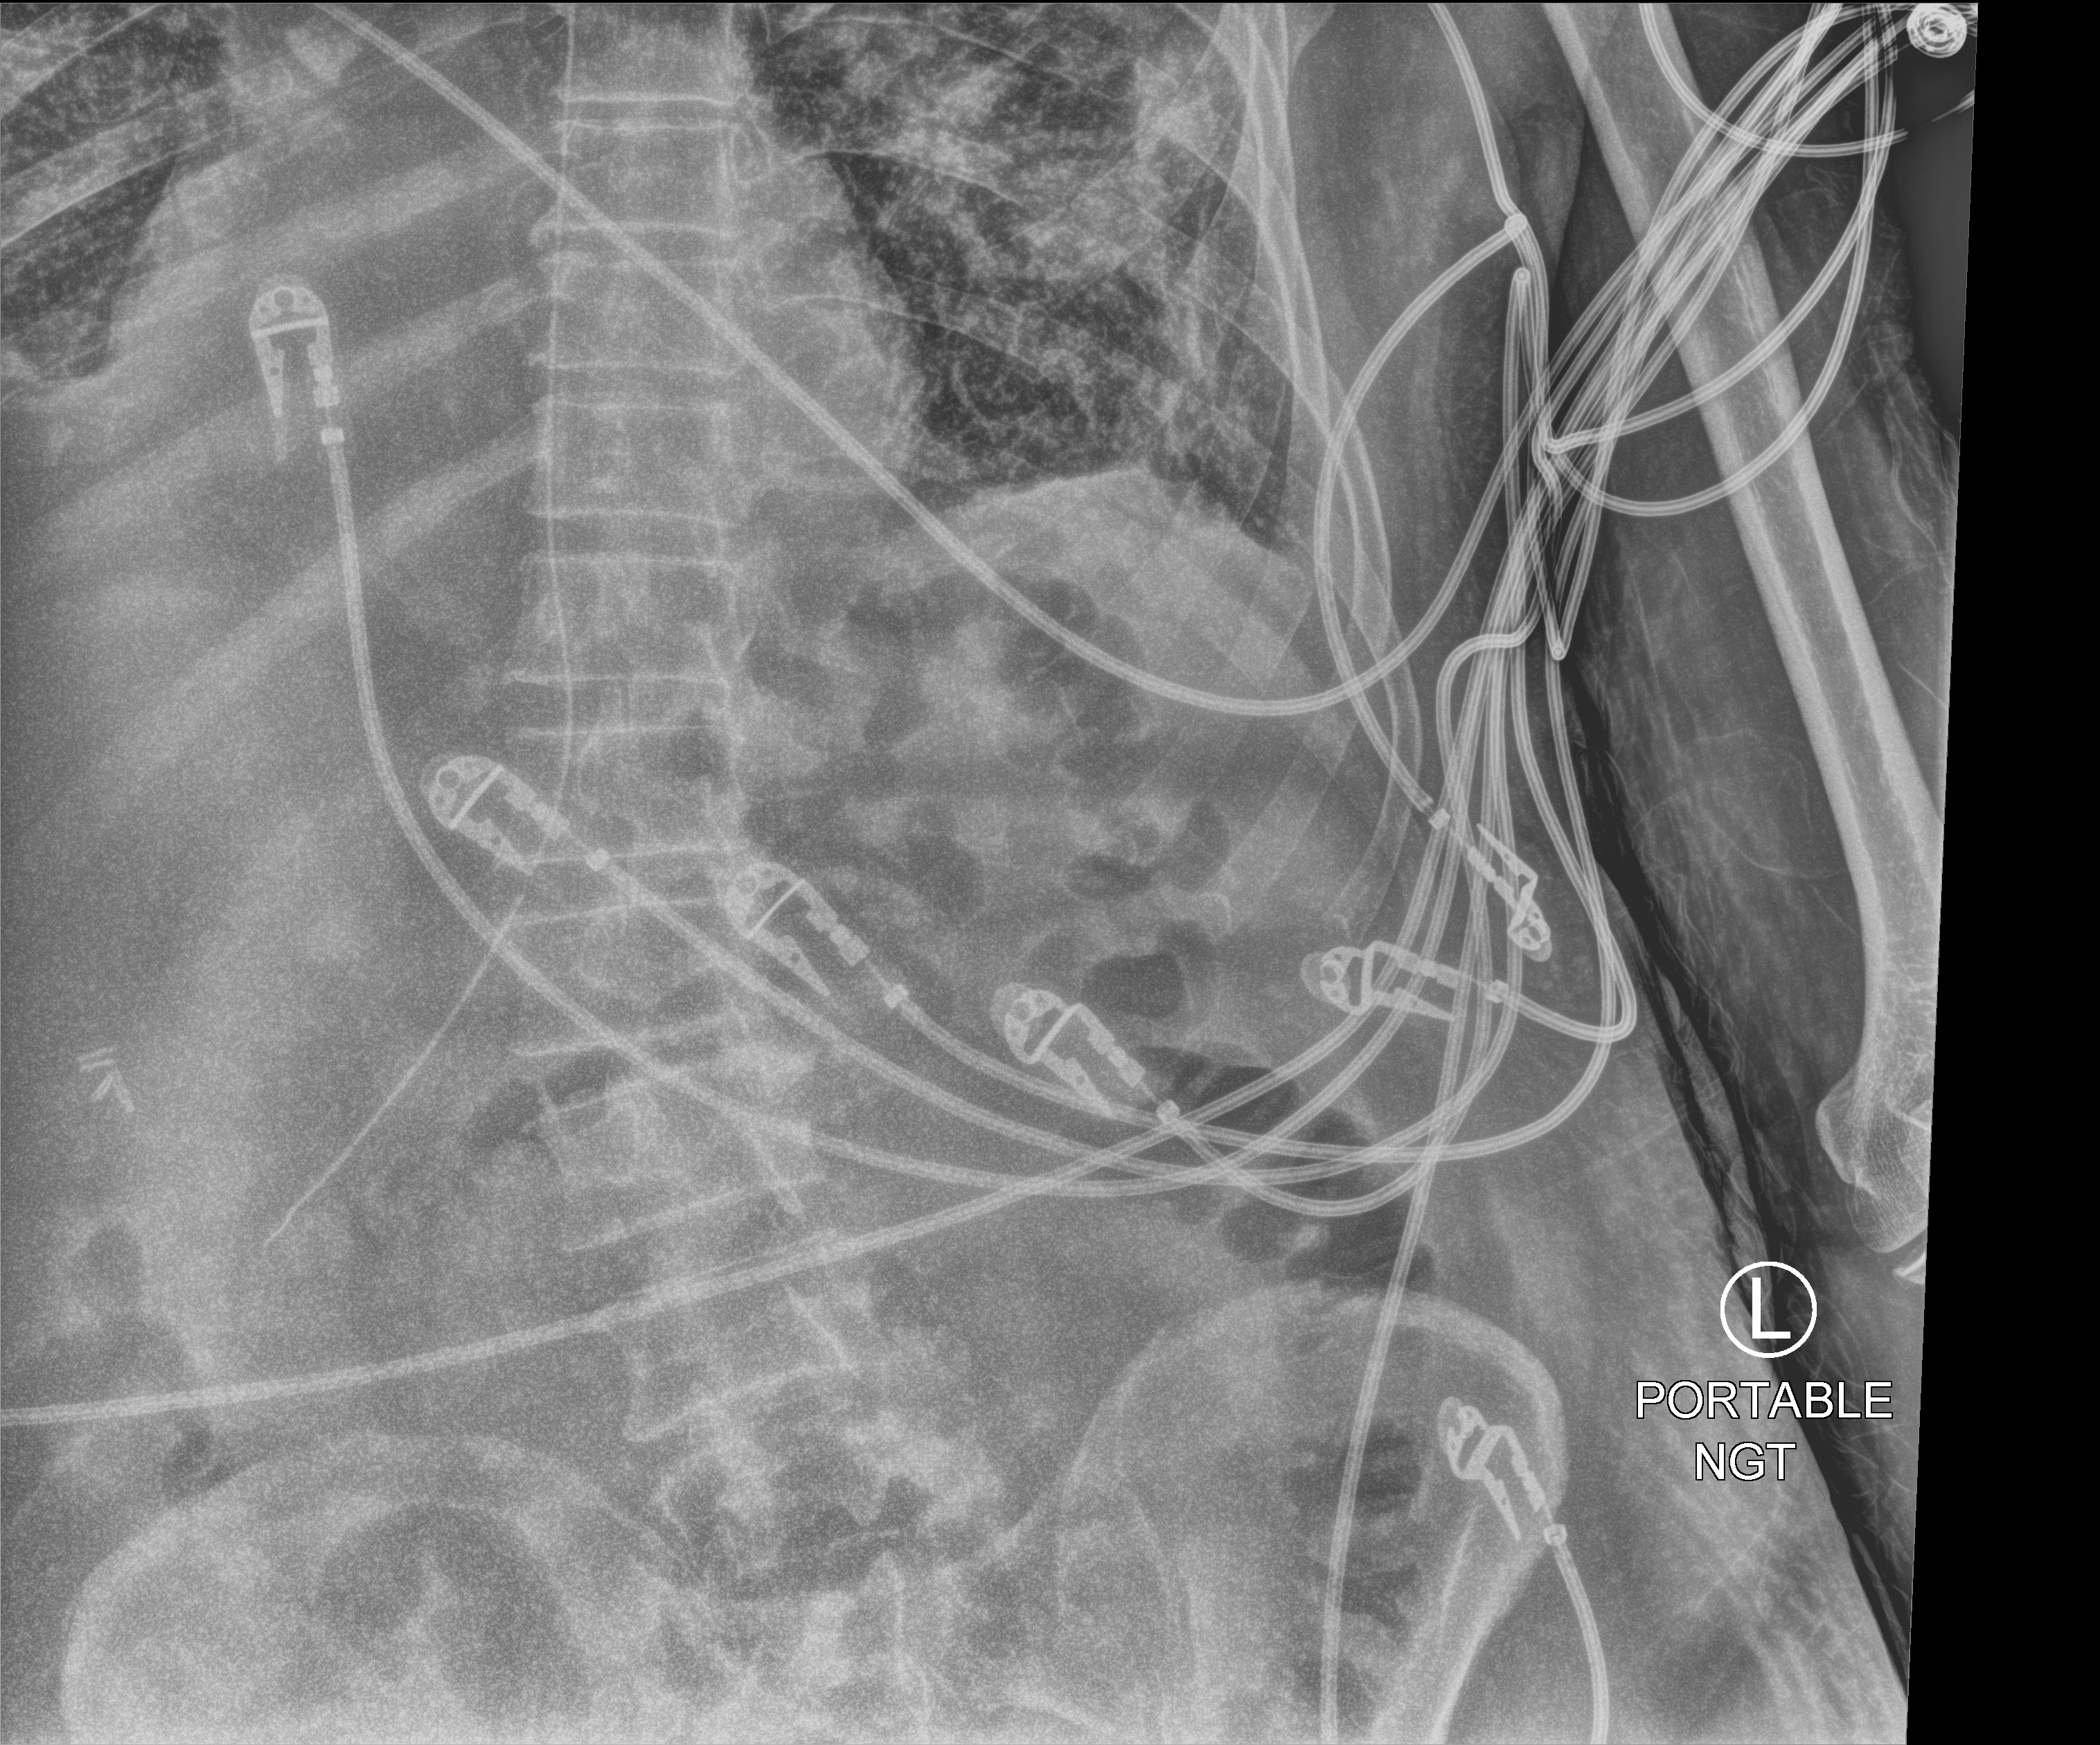
Bedside chest radiograph (computed radiography), anteroposterior (AP) projection. Male patient hospitalised with COVID-19, age 75–90 years.
From the hospital-stay record, not from the radiograph (when in the stay this image was taken is not recorded): hypertension (admission record): no; mechanically ventilated during this hospital stay: yes; admitted to intensive care during this hospital stay: yes.